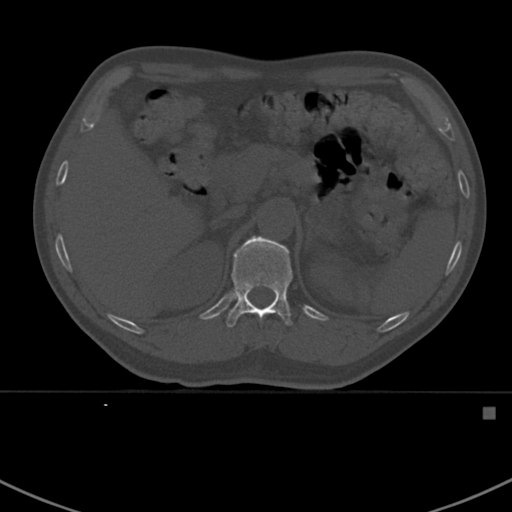
CT including the spine, one axial slice. Position 330 of 412 along the scan axis. Reconstruction kernel Br40s. 120 kVp. Bone window (W 1800 / L 400 HU). 1.5 mm slice thickness. 512 × 512 image matrix, field of view 358 × 358 mm. Patient: male, 59 years. From the clinical record (not read from this slice): primary cancer: prostate.
Annotated regions visible in this slice (semi-automatic segmentation, software-assisted and operator-edited):
- T12 vertebra: box from (x=226, y=236) to (x=293, y=327) px